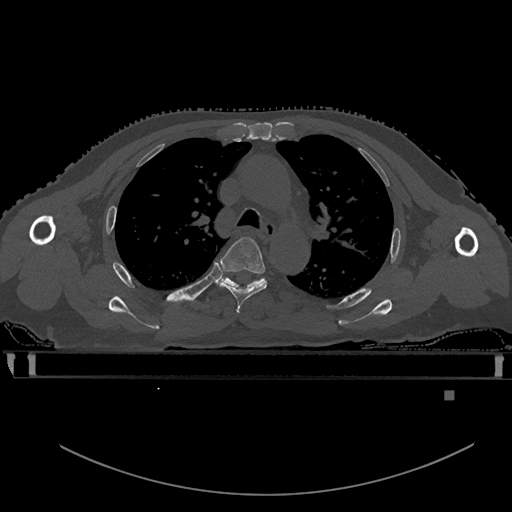
CT including the spine, one axial slice; slice 393 of 969 in the series (ordered by position); bone window (W 1800 / L 400 HU); 0.5 mm slice thickness; 512 × 512 image matrix, field of view 456 × 456 mm. Patient: male, 82 years. From the clinical record (not read from this slice): primary cancer: prostate.
Outlined on this slice (semi-automatically segmented with operator editing):
- T4 vertebra: box from (x=216, y=236) to (x=267, y=312) px
- T5 vertebra: (x=217, y=274)–(x=265, y=287)